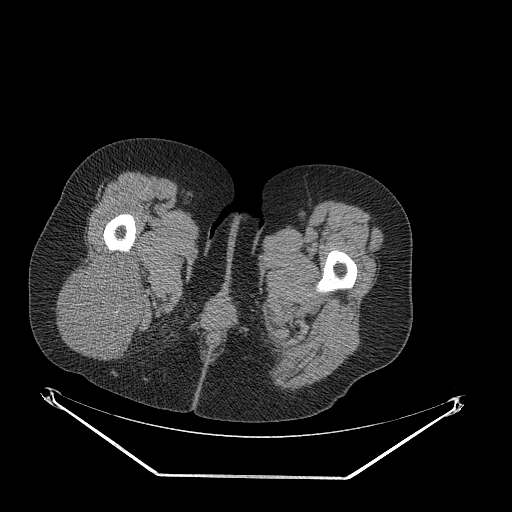
CT of an extremity soft-tissue mass (from a PET/CT study), one axial slice. Slice 49 of 257 in the series (ordered by position). Reconstruction kernel STANDARD. 140 kVp. Soft-tissue window (W 400 / L 40 HU). 512 × 512 image matrix. Female patient. Case-level facts recorded for this patient, not image findings: histological type: synovial sarcoma; grade: intermediate; site of the primary tumour: right buttock.
Outlined on this slice (expert contour drawn on MRI and transferred to this co-registered scan by the dataset authors):
- gross tumour volume including surrounding oedema: bounding box <66,253,147,350> (left, top, right, bottom; pixels)
- gross tumour volume (mass): <66,254,147,350>